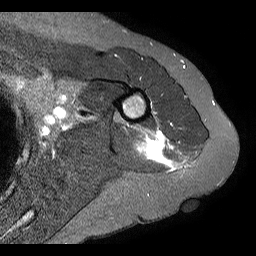
MRI of an extremity soft-tissue mass, one axial slice; position 4 of 20 along the scan axis; STIR; 256 × 256 image matrix, field of view 150 × 150 mm. Female patient. From the clinical record (not read from this slice): histological type: malignant fibrous histiocytoma; grade: low; site of the primary tumour: left arm.
Structures marked on this image (outlined manually by an expert reader):
- gross tumour volume (mass): bounding box (x1, y1, x2, y2) in pixels: (134, 133, 166, 166)